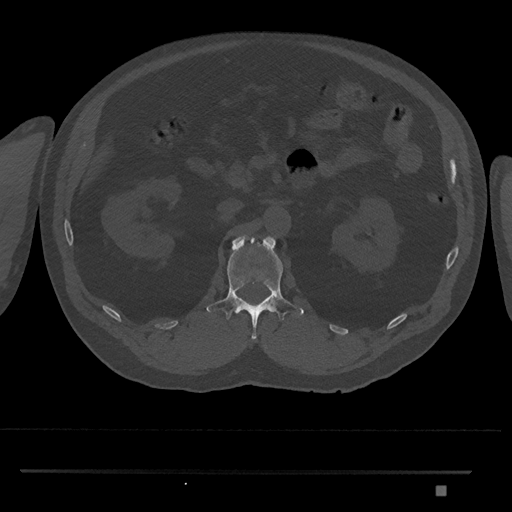
CT including the spine, one axial slice. Slice 820 of 1134 in the series (ordered by position). 120 kVp. Bone window (W 1800 / L 400 HU). 0.5 mm slice thickness. 512 × 512 image matrix, field of view 429 × 429 mm. Male patient, age 65 years. Case-level facts recorded for this patient, not image findings: primary cancer: prostate.
Structures marked on this image (semi-automatically segmented with operator editing):
- L1 vertebra: bounding box <206,234,304,340> (left, top, right, bottom; pixels)